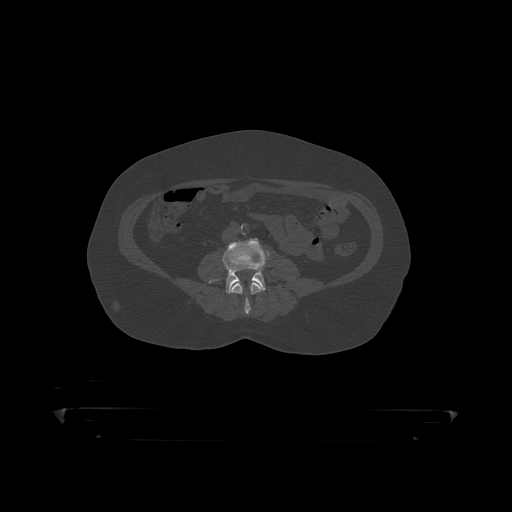
CT including the spine, one axial slice; position 75 of 390 along the scan axis; bone window (W 1800 / L 400 HU); 512 × 512 image matrix, field of view 650 × 650 mm. Male patient, age 60 years. Case-level facts recorded for this patient, not image findings: primary cancer: prostate.
Annotated regions visible in this slice (semi-automatic segmentation, software-assisted and operator-edited):
- L3 vertebra: bounding box (x1, y1, x2, y2) in pixels: (230, 281, 264, 315)
- L4 vertebra: (210, 239, 269, 294)